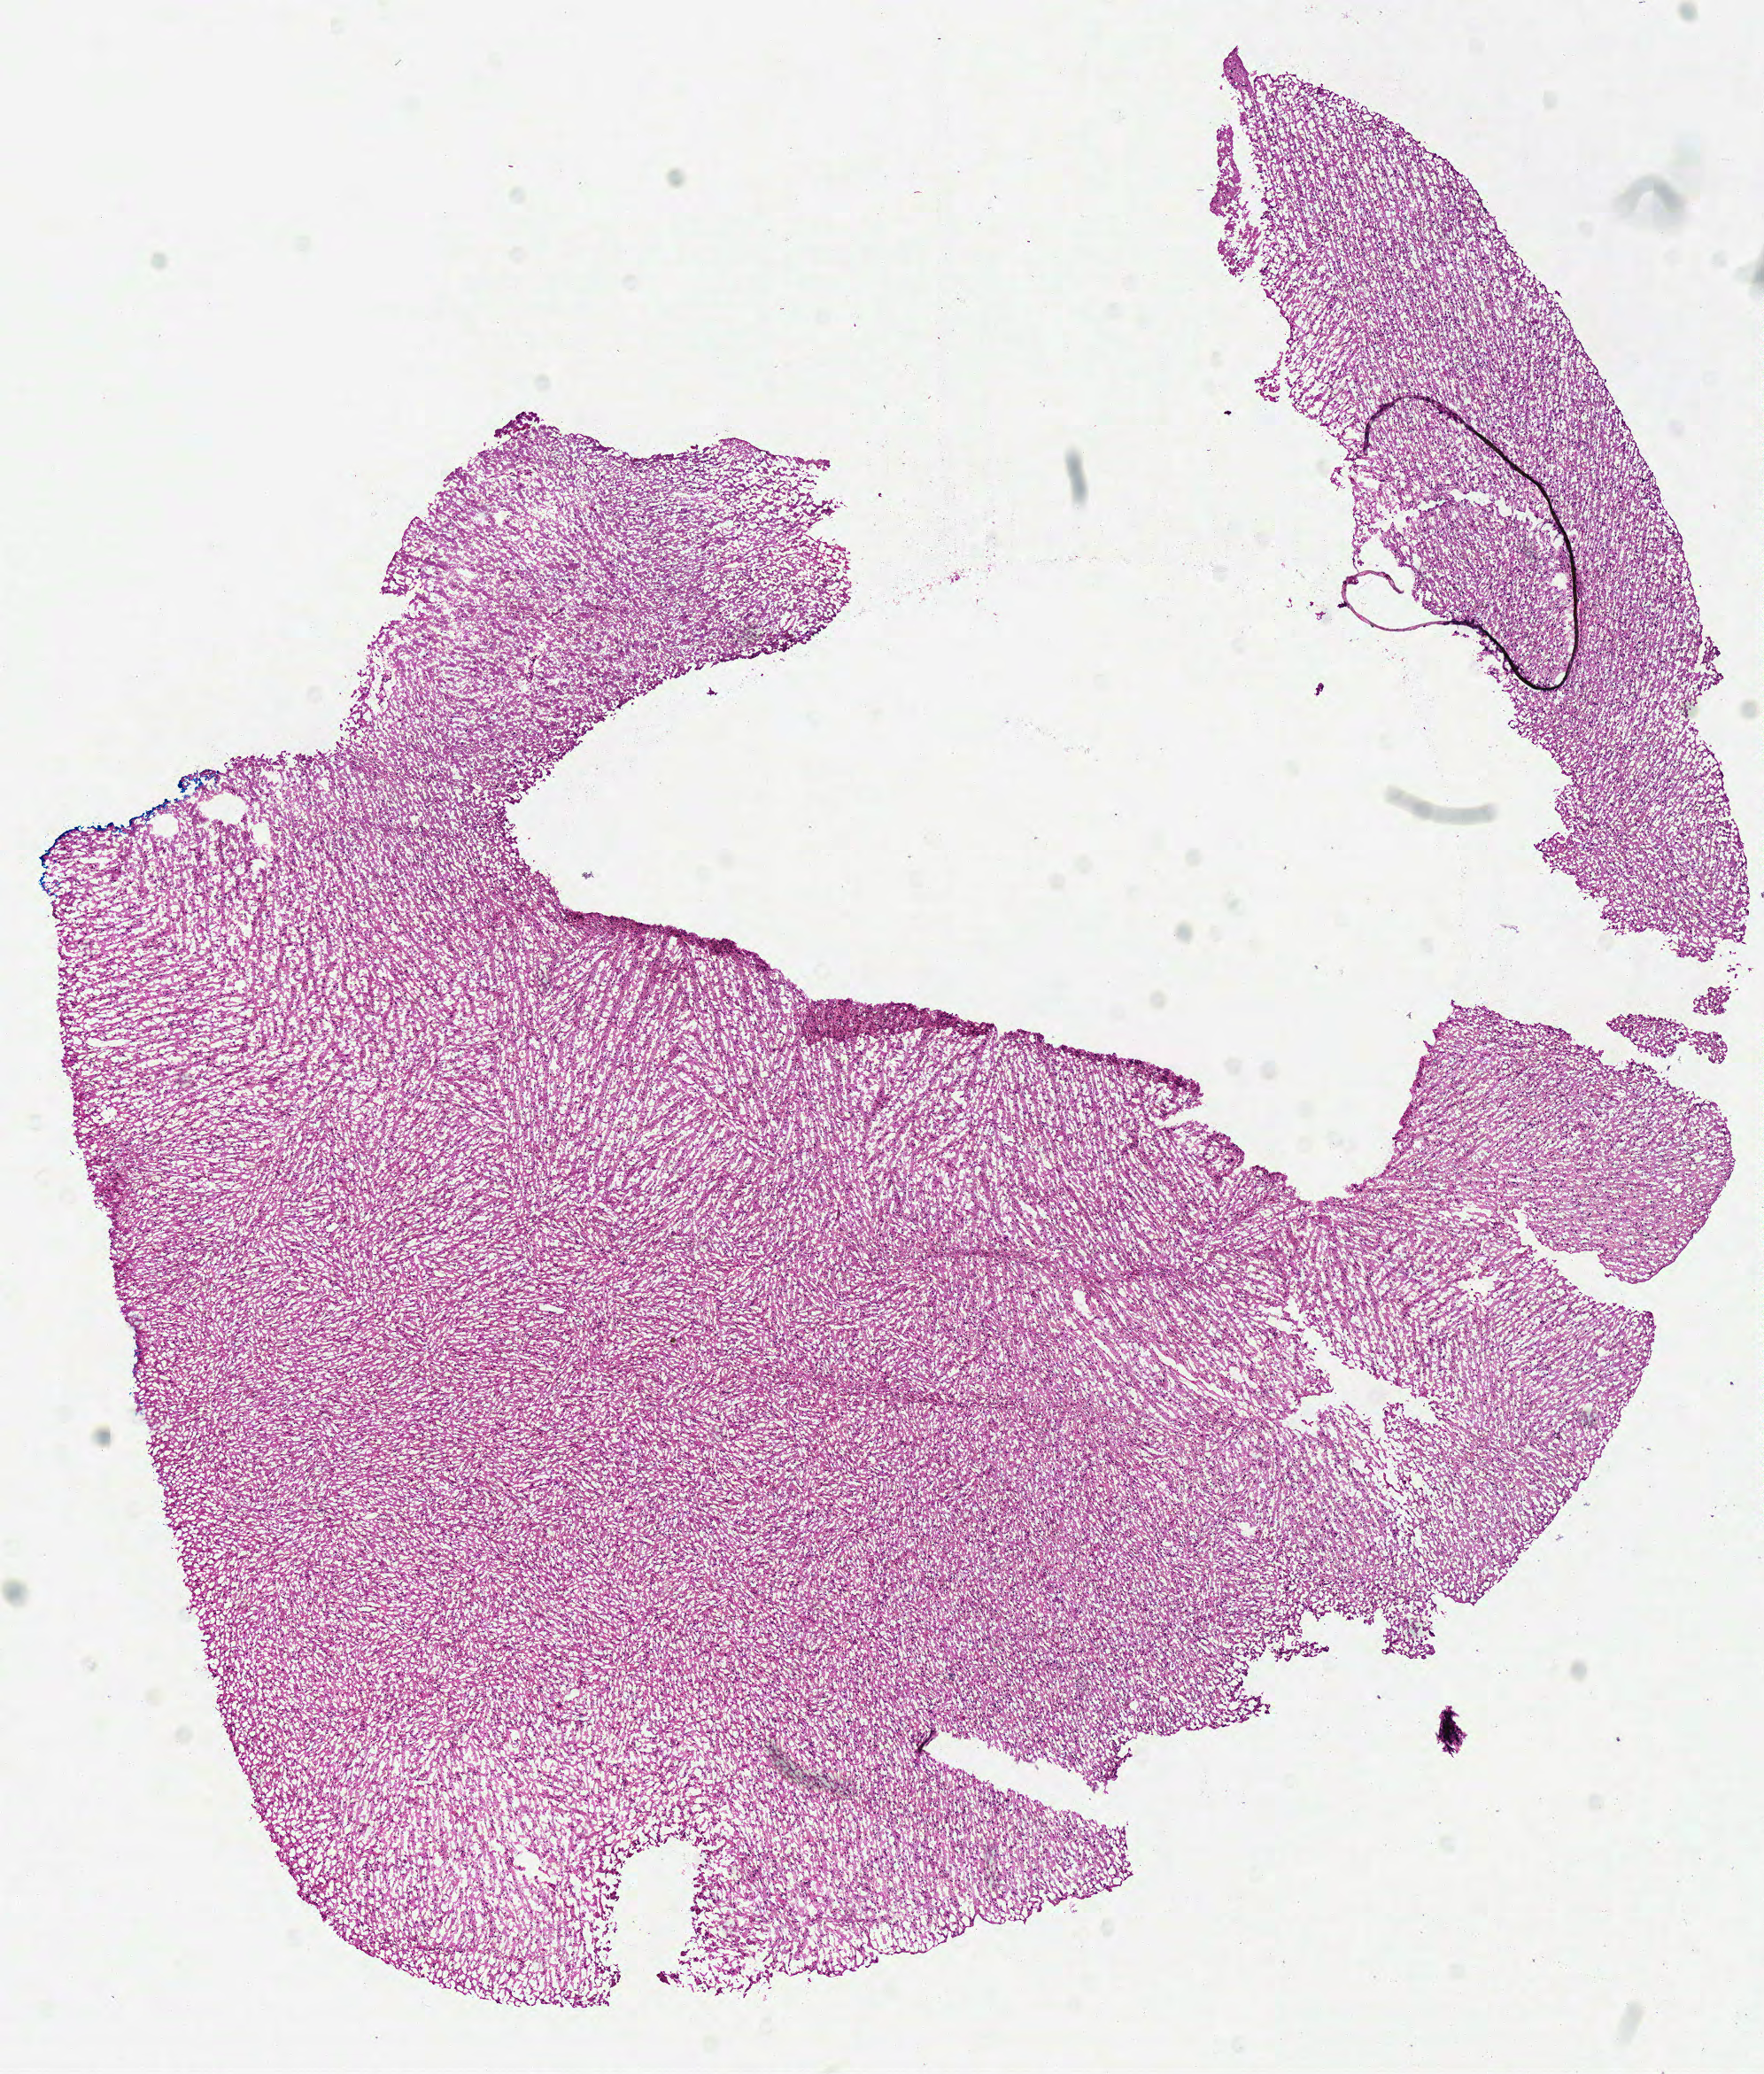
Digitized Hematoxylin and eosin (H&E) stained tissue section (whole slide) — low-resolution overview of the scanned area, about 7.8 x 9.2 mm (slide scanned at 40x). Frozen section. Sample: primary tumour, brain. Male, age 58 years at initial diagnosis. Slide review estimates, as recorded: tumour cells 100%, tumour nuclei 70%, normal cells 0%, stromal cells 0%, necrosis 0%.
Pathologic diagnosis: Glioblastoma.